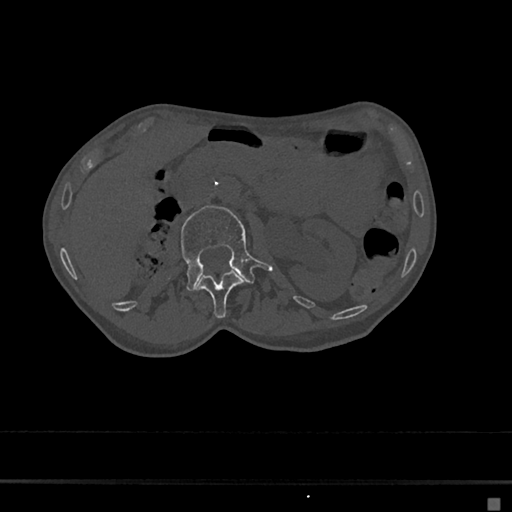
CT including the spine, one axial slice. 120 kVp. Bone window (W 1800 / L 400 HU). 0.5 mm slice thickness. 512 × 512 image matrix, field of view 360 × 360 mm. Patient: female, 68 years. Case-level facts recorded for this patient, not image findings: primary cancer: renal.
Annotated regions visible in this slice (semi-automatically segmented with operator editing):
- L1 vertebra: bounding box [x1, y1, x2, y2] px = [196, 270, 244, 319]
- L2 vertebra: [180, 205, 272, 291]